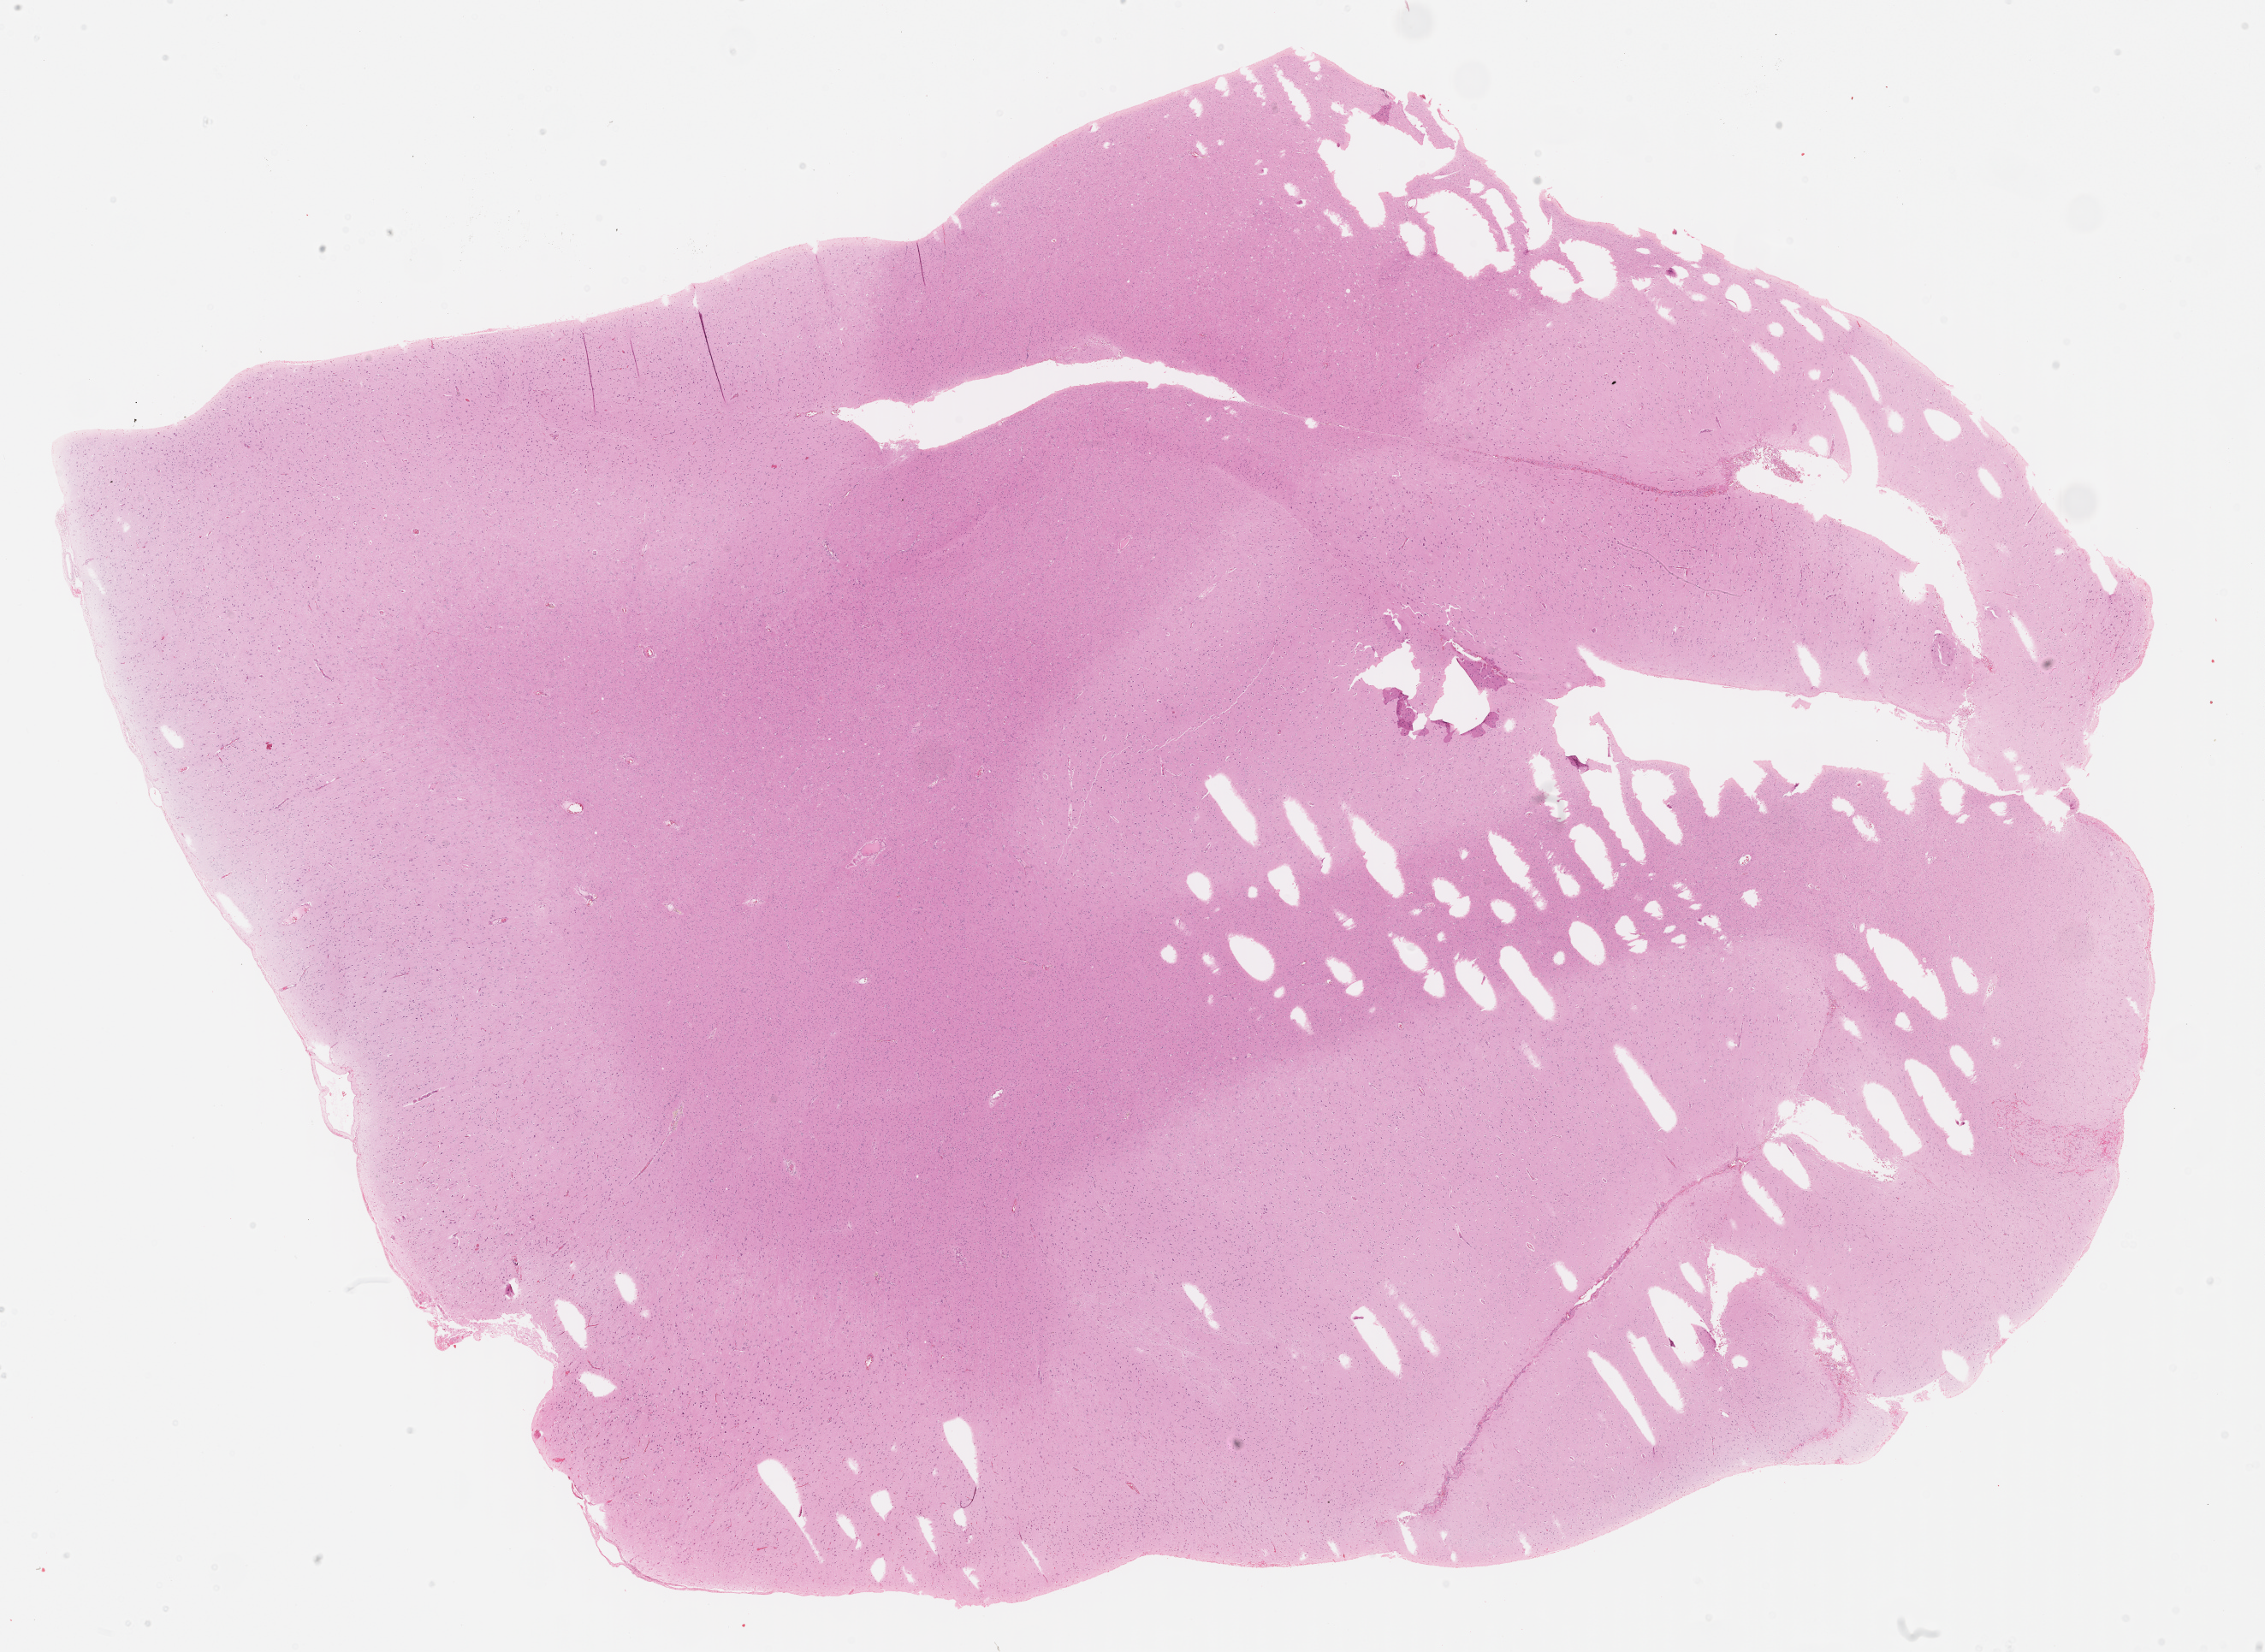
Hematoxylin and eosin (H&E) stained whole-slide image, a low-resolution overview of the entire scanned area, about 21.3 x 15.6 mm (acquisition: 40x scan). FFPE section. Brain, primary tumour sample. Male patient; age at initial diagnosis 40 years. Histologic grade: G2 (moderately differentiated).
Pathologic diagnosis: Oligodendroglioma, NOS (cerebrum). Laterality: right.